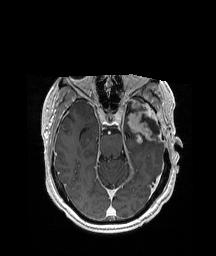
Brain MRI from a brain-tumour surgery series, one axial slice; position 129 of 208 along the scan axis; T1-weighted post-contrast; 1 mm slice thickness; 216 × 256 image matrix. Case-level facts recorded for this patient, not image findings: histopathology: Glioblastoma; WHO grade: 4; IDH mutation: no; tumour location: Left Anterior/Superior Temporal.
Annotated regions visible in this slice (expert manual segmentation):
- previous resection cavity: bounding box <140,116,159,135> (left, top, right, bottom; pixels)
- tumour: <123,99,158,144>